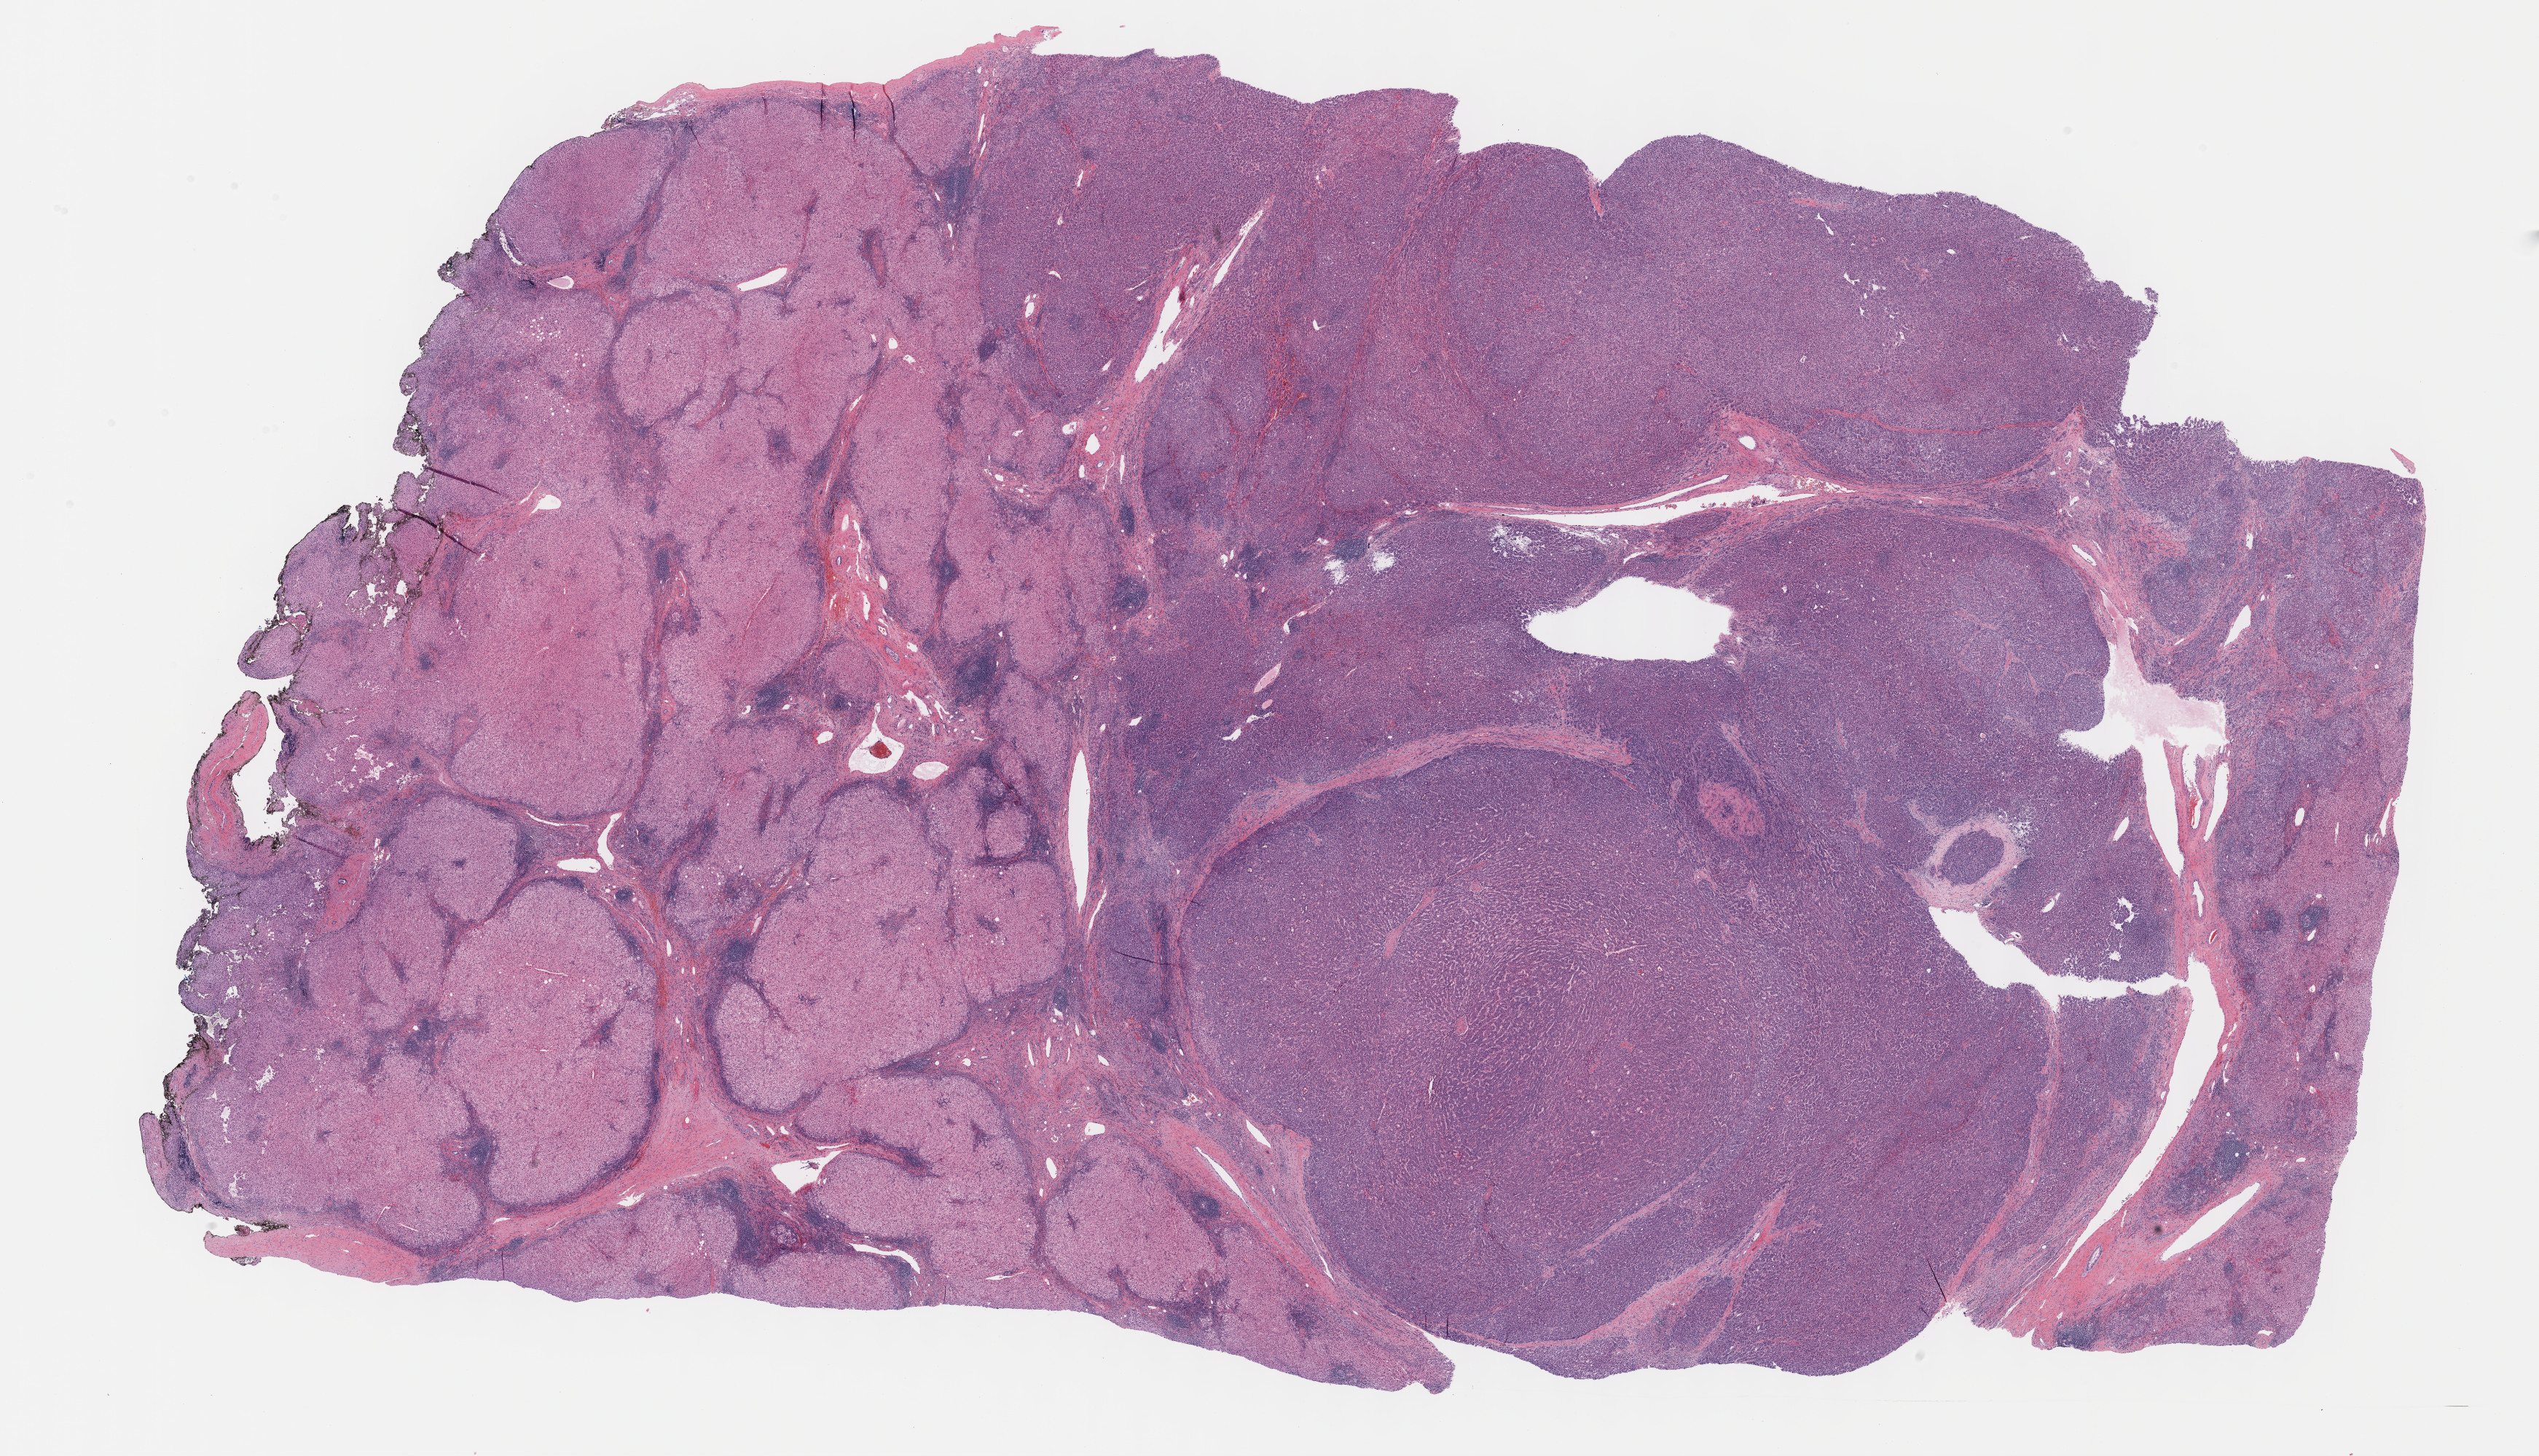
H&E-stained whole-slide image — a low-resolution overview of the entire scanned area, about 28.2 x 16.2 mm, formalin-fixed paraffin-embedded (FFPE) diagnostic section, primary tumour sample from the liver. Male, age 77 years at initial diagnosis.
* histologic diagnosis: Hepatocellular carcinoma, NOS